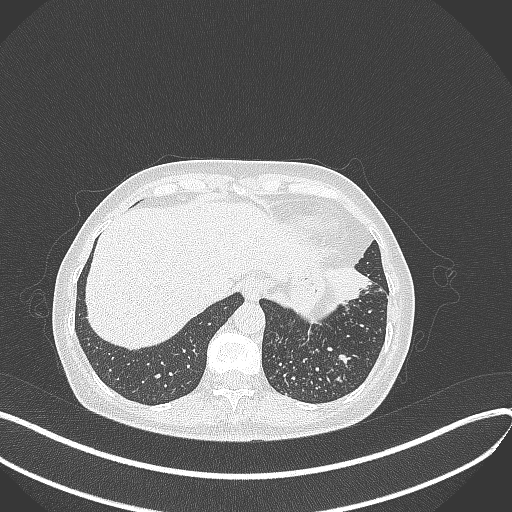
Chest CT, one axial slice. Position 82 of 429 along the scan axis. Lung window (W 1500 / L -600 HU). 512 × 512 image matrix, field of view 400 × 400 mm. Patient: female, 63 years. From the clinical record (not read from this slice): clinical TNM (as recorded): T1b N0 M0; histopathological grade: G2-3.
Structures marked on this image (bounding box drawn by a radiologist):
- lung tumour (recorded histology: adenocarcinoma): box from (x=323, y=263) to (x=379, y=307) px